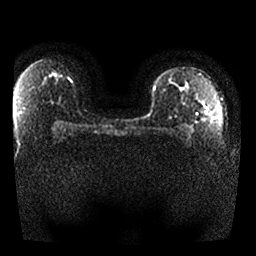
Breast MRI, one axial slice; position 19 of 25 along the scan axis; diffusion-weighted series; image 2 of 4 stored at this slice position (different b-values; order by instance number); 1.5 T; 4 mm slice thickness; 256 × 256 image matrix. Female patient.
Annotated regions visible in this slice (manually delineated by an expert):
- tumour on diffusion-weighted imaging: bounding box <181,86,185,91> (left, top, right, bottom; pixels)